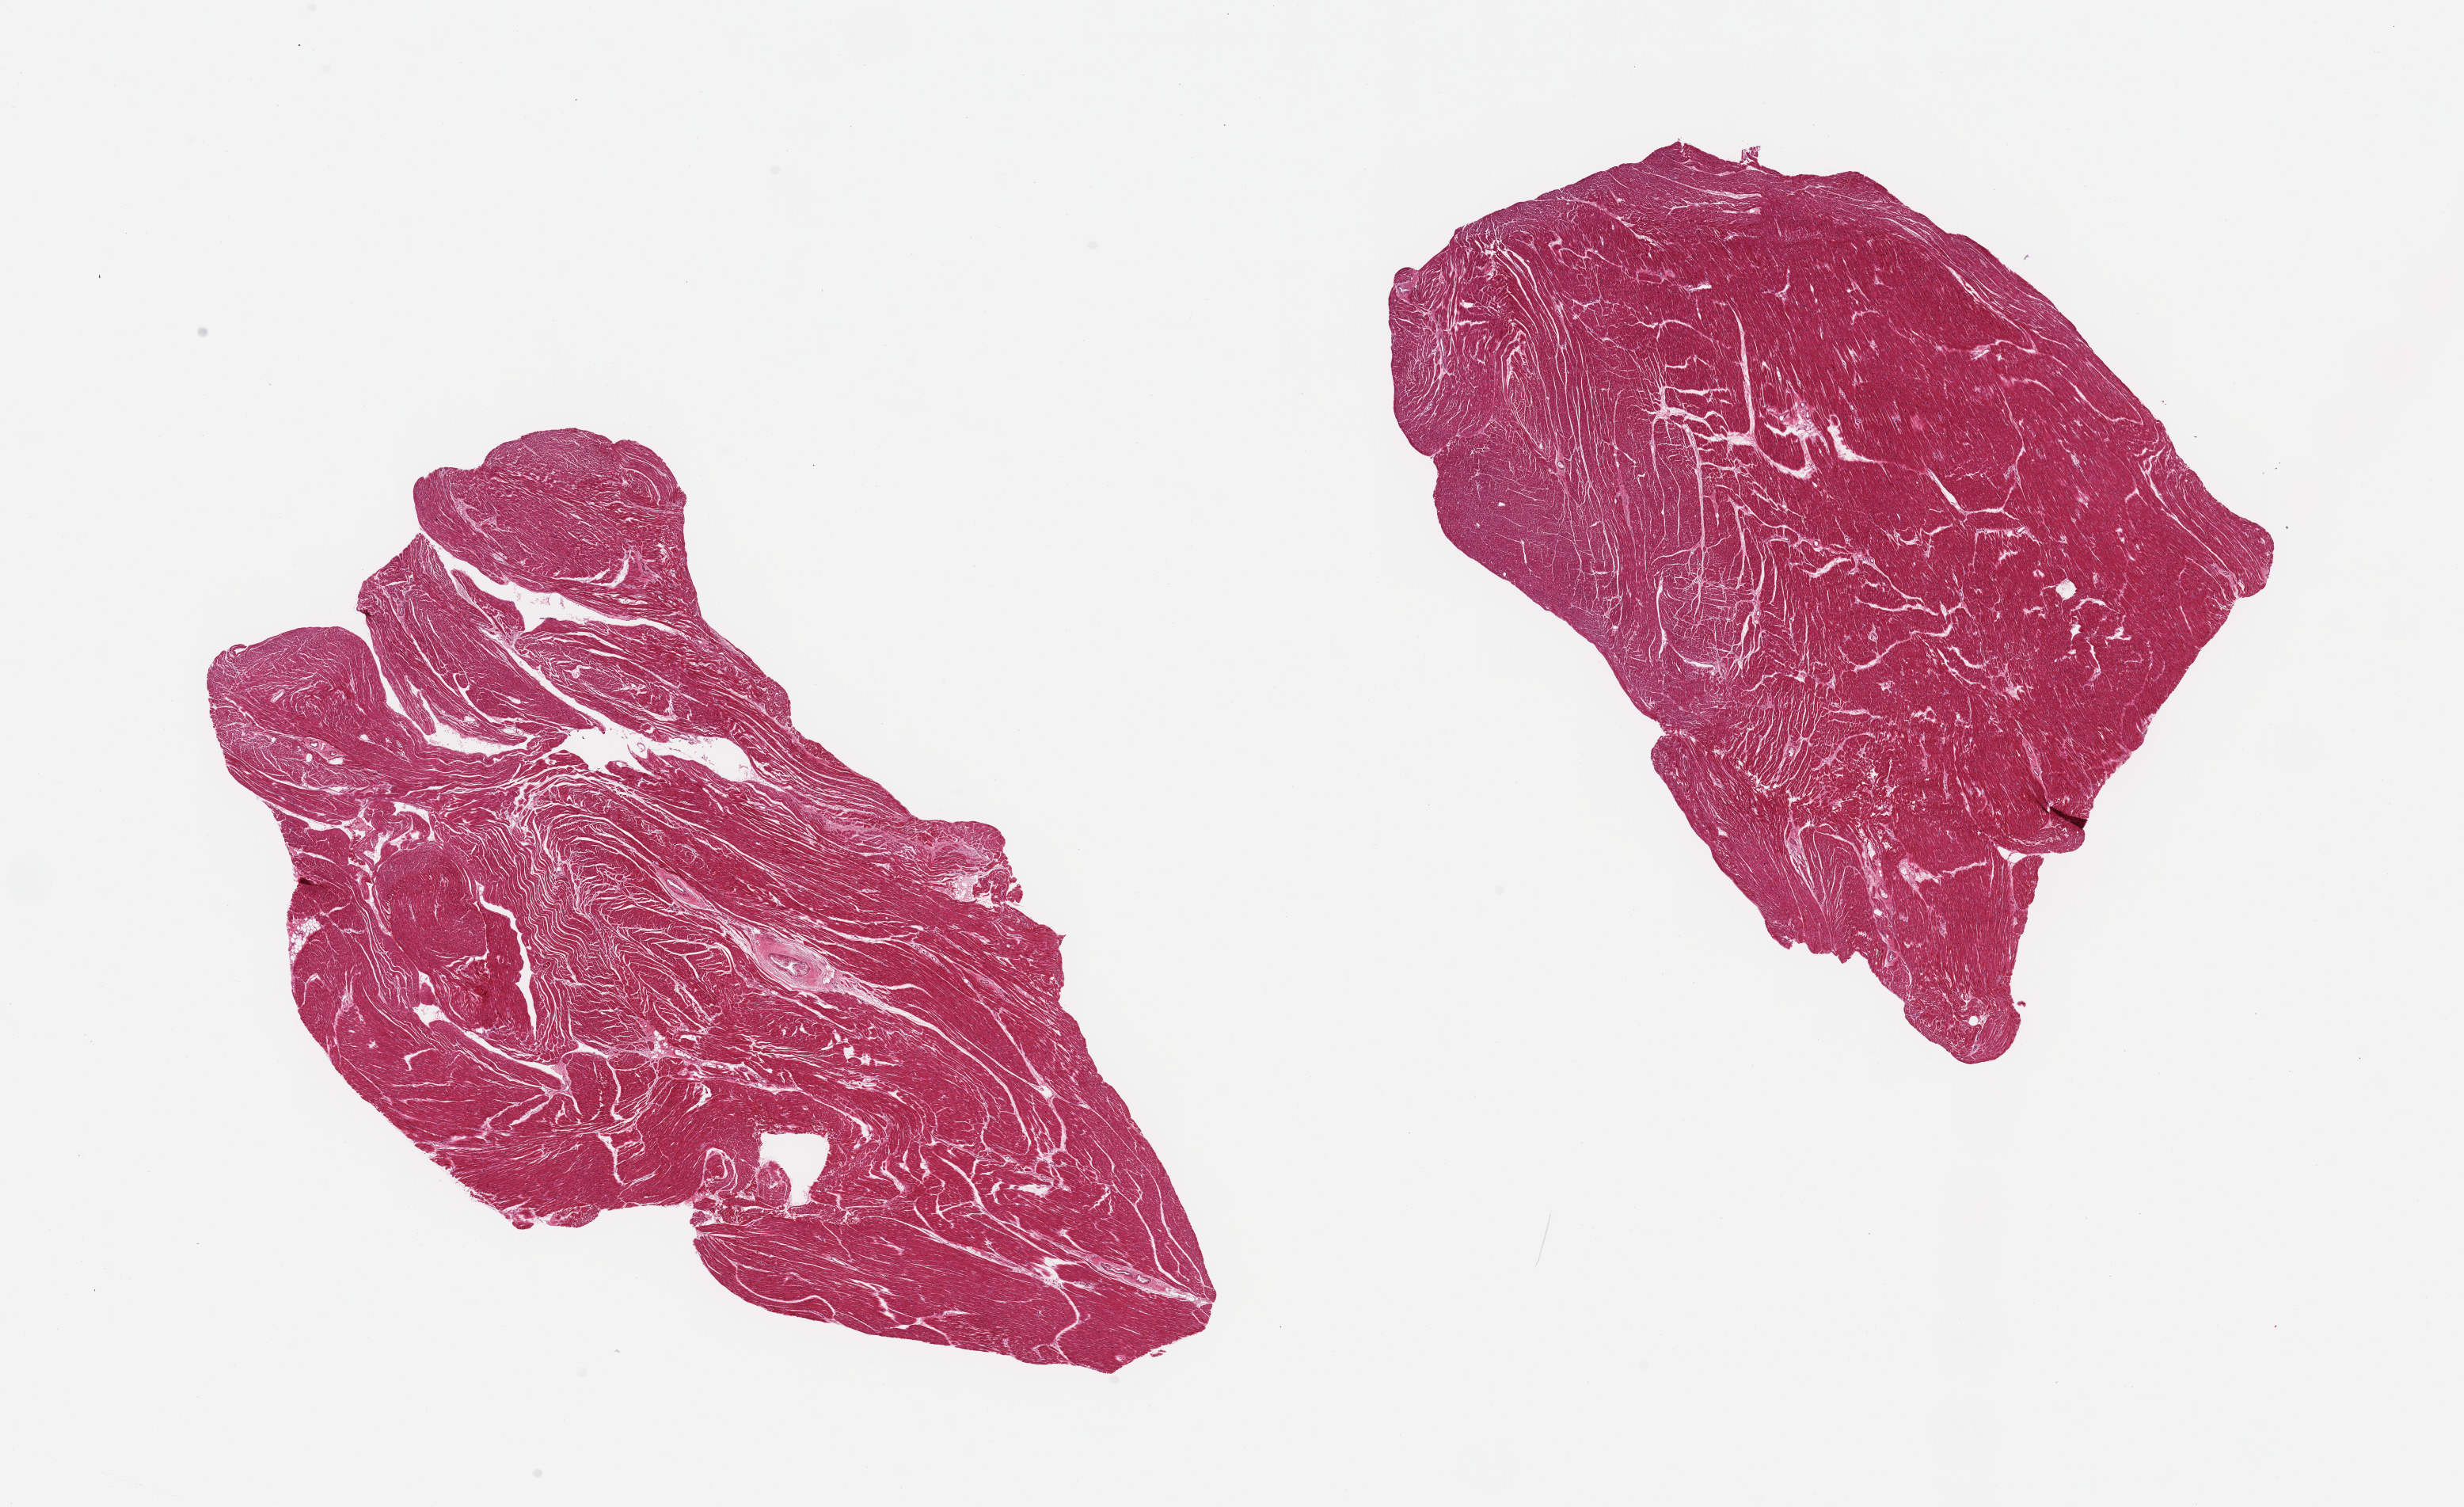
Haematoxylin and eosin whole-slide image, brightfield, shown as a low-resolution overview of the whole scanned area (about 24.6 x 15.0 mm, acquisition: 20x scan), PAXgene-fixed, paraffin-embedded tissue, sampled site (target tissue): heart, donor tissue sample. Donor: male.
Pathologist's review note for this sample: 2 pieces, minimal mild ischemic changes/interstitial fibrosis.